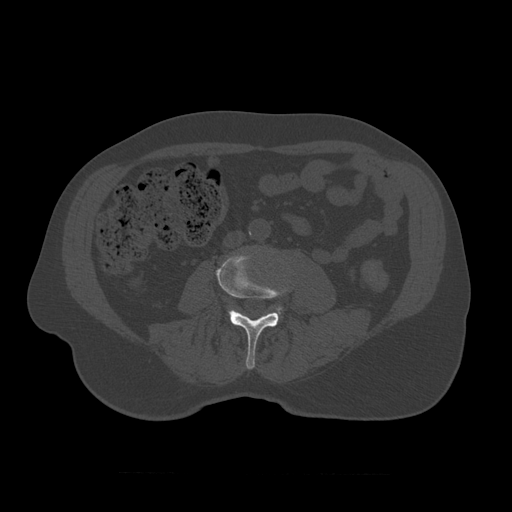
CT including the spine, one axial slice; slice 296 of 450 in the series (ordered by position); reconstruction kernel STANDARD; bone window (W 1800 / L 400 HU); 1.25 mm slice thickness; 512 × 512 image matrix. Patient age 75 years. From the clinical record (not read from this slice): primary cancer: prostate.
Structures marked on this image (semi-automatic segmentation, software-assisted and operator-edited):
- L3 vertebra: bounding box (x1, y1, x2, y2) in pixels: (216, 252, 288, 370)
- L4 vertebra: (231, 283, 283, 312)